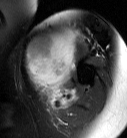
MRI of an extremity soft-tissue mass, one axial slice; position 54 of 87 along the scan axis; T2-weighted fat-saturated; MR volume resampled by the dataset authors to the PET/CT grid (not the native acquisition matrix); 3.27 mm slice thickness; 127 × 138 image matrix, field of view 124 × 135 mm. Female patient. Case-level facts recorded for this patient, not image findings: histological type: pleiomorphic leiomyosarcoma; grade: high; site of the primary tumour: left biceps.
Structures marked on this image (expert contour drawn on MRI and transferred to this co-registered scan by the dataset authors):
- gross tumour volume including surrounding oedema: bounding box <25,29,80,106> (left, top, right, bottom; pixels)
- gross tumour volume (mass): <25,29,78,90>